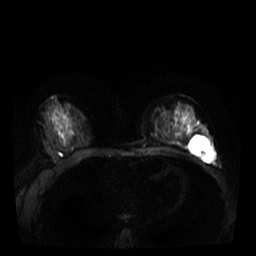
Breast MRI, one axial slice; slice 19 of 40 in the series (ordered by position); diffusion-weighted series; image 2 of 4 stored at this slice position (different b-values; order by instance number); 3 T; 5 mm slice thickness; 256 × 256 image matrix. Female patient.
Outlined on this slice (manually delineated by an expert):
- tumour on diffusion-weighted imaging: bounding box (x1, y1, x2, y2) in pixels: (199, 151, 215, 162)